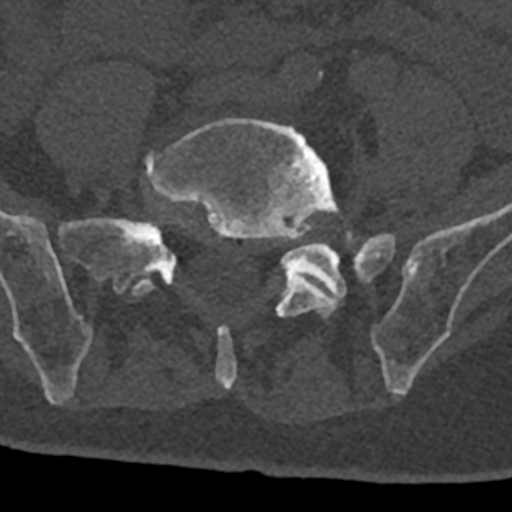
CT including the spine, one axial slice. Slice 179 of 797 in the series (ordered by position). Reconstruction kernel Br40s/3. 120 kVp. Bone window (W 1800 / L 400 HU). 512 × 512 image matrix. Male patient, age 74 years. From the clinical record (not read from this slice): primary cancer: renal; vertebrae with lytic lesions (as recorded): T10, L1, L2, L3, L4, L5.
Outlined on this slice (semi-automatic segmentation, software-assisted and operator-edited):
- L4 vertebra: box from (x=318, y=72) to (x=322, y=79) px
- L5 vertebra: (x=132, y=118)–(x=354, y=389)